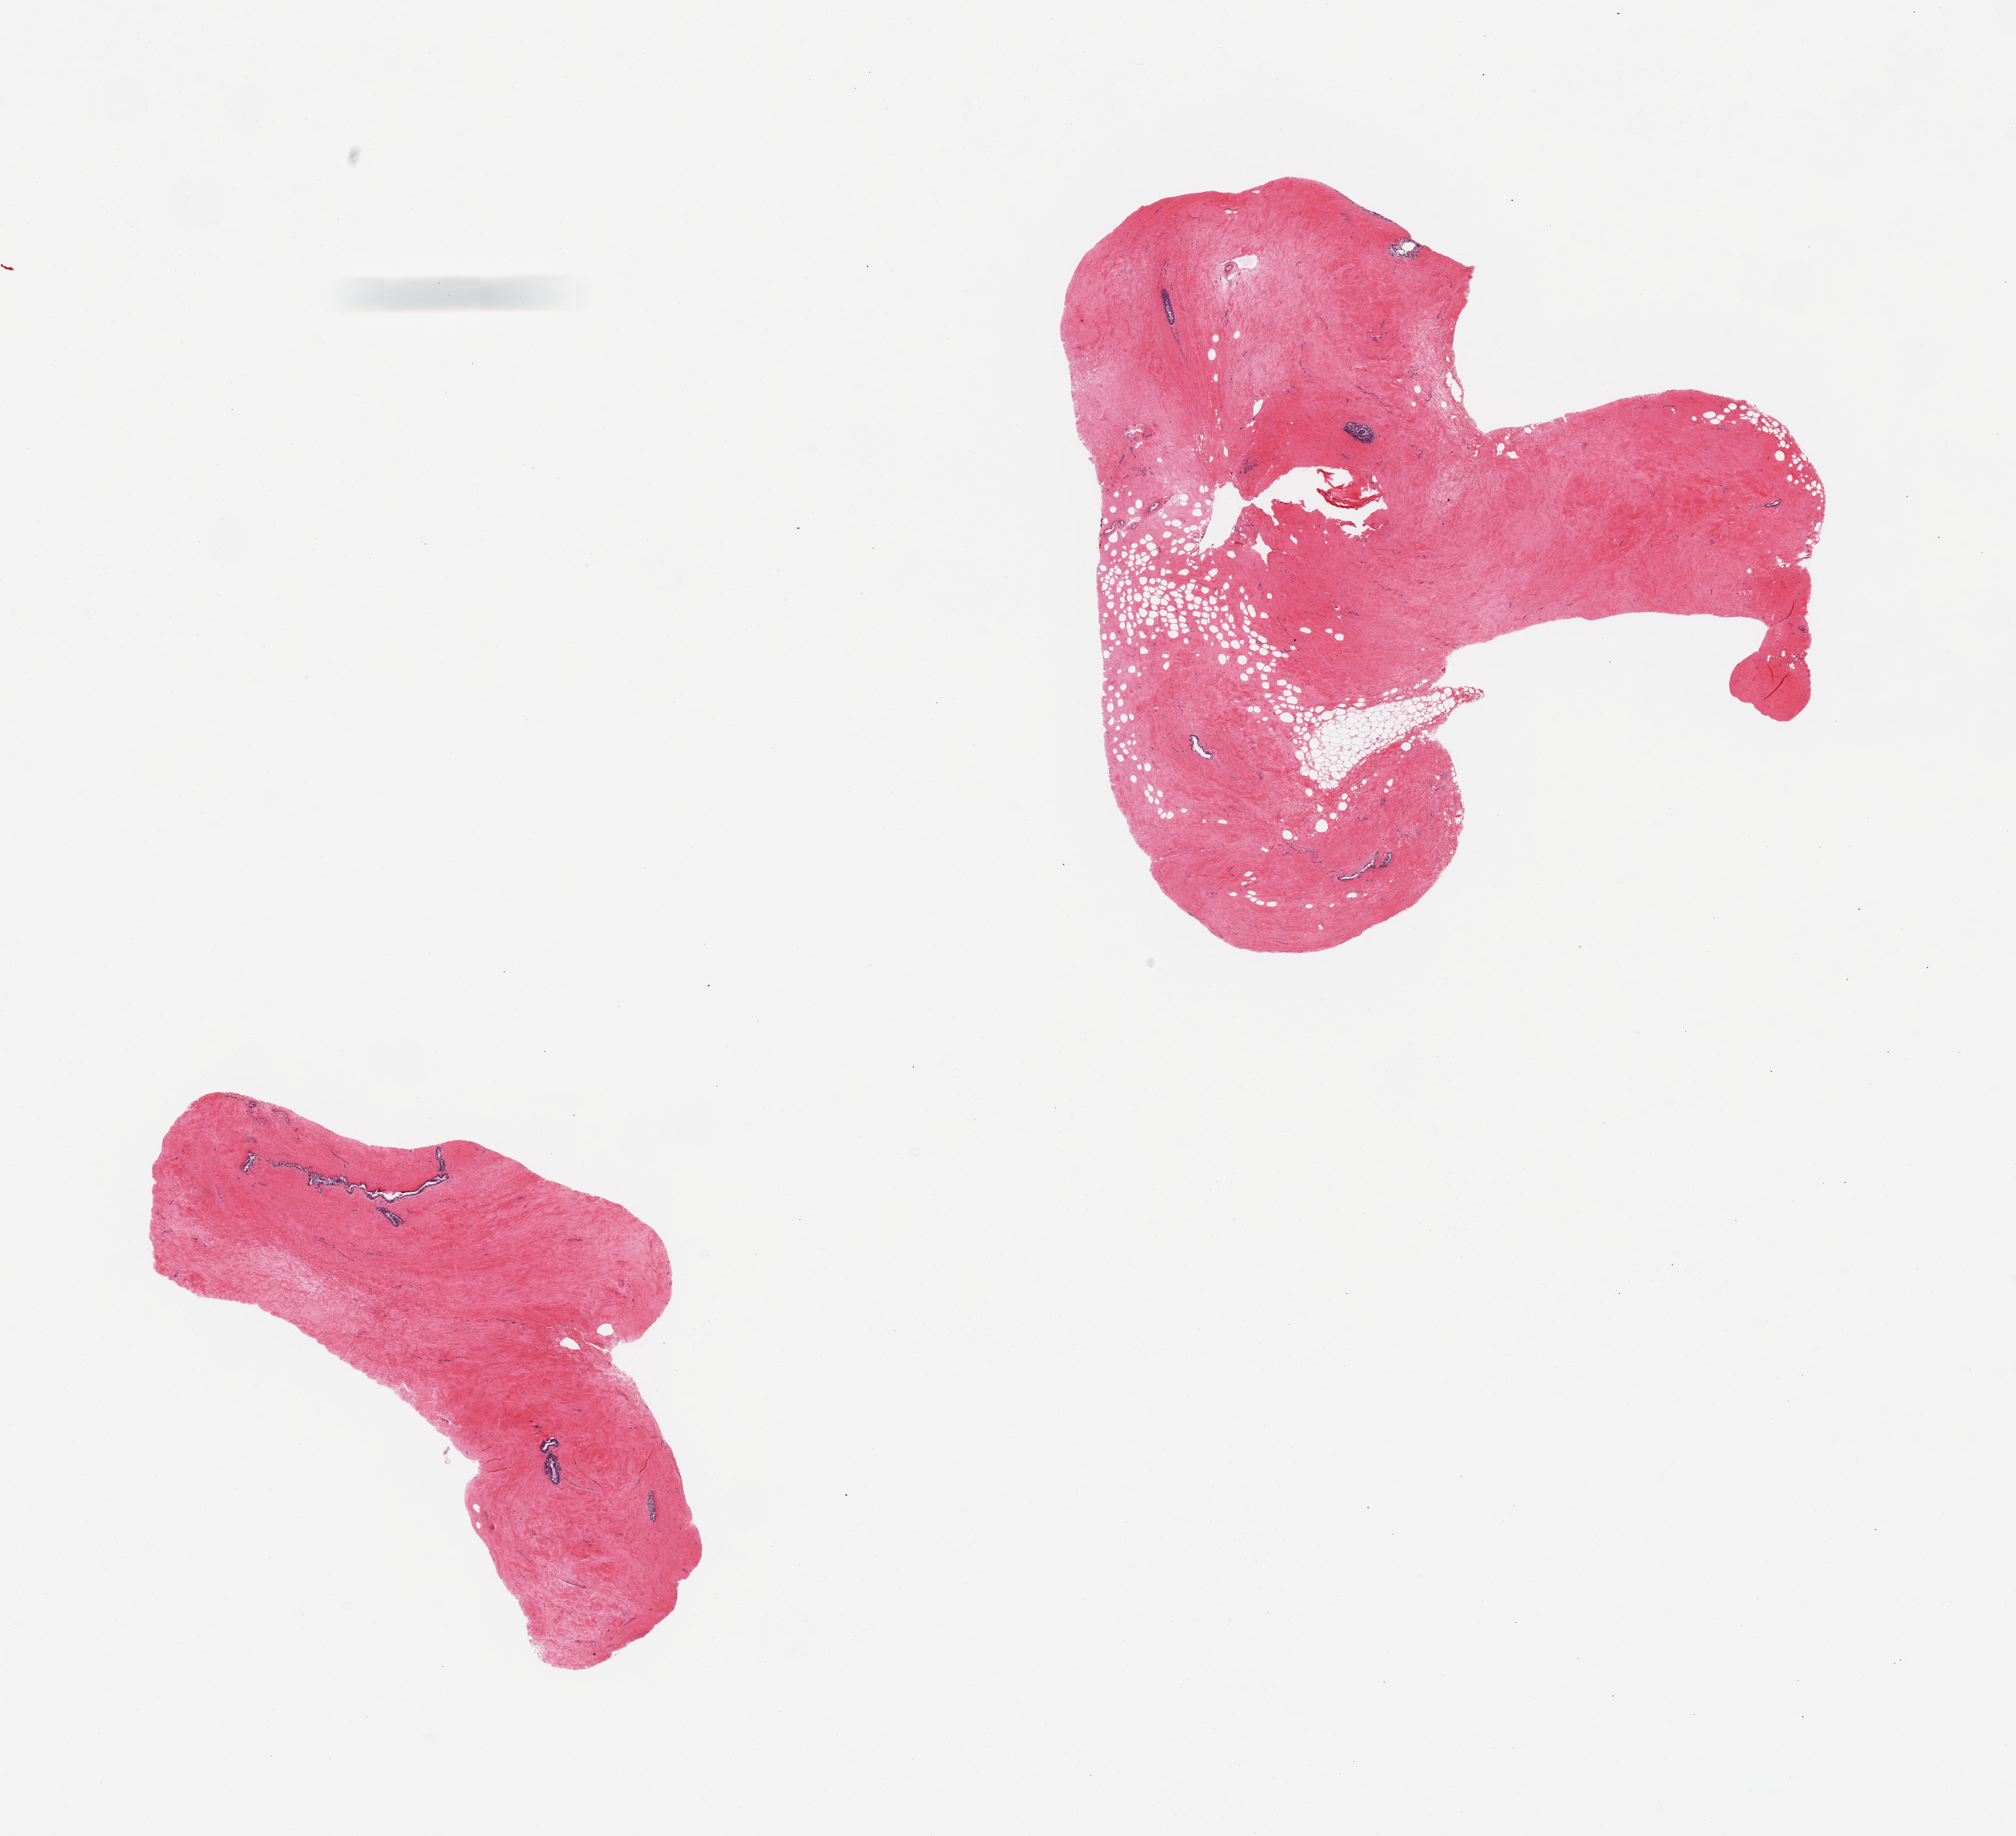
Whole-slide image, hematoxylin and eosin (H&E) stain, brightfield — low-resolution overview of the scanned area, about 20.7 x 18.8 mm (from a 20x scan); PAXgene-fixed, paraffin-embedded tissue; target tissue: breast; tissue donor sample. Donor: male.
• review note (as recorded): 2 pieces; gynecomastoid changes